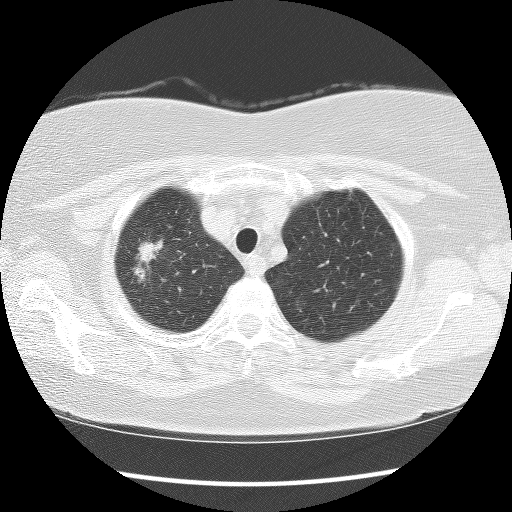
Axial slice from a low-dose chest CT screening exam; second screening round (one year after baseline); lung window (W 1500 / L -600 HU); 120 kVp; slice 5 of 79 in the series. Female participant, aged 67 years at enrolment.
- Expert reader's lesion annotation, bounding box <114,231,173,293> (left, top, right, bottom; pixels).
- The screening reader recorded 3 non-calcified nodules or masses ≥4 mm on this exam; which of them this box marks is not recorded.
- Later outcome: lung cancer diagnosed 56 days after this screen — adenocarcinoma with mixed subtypes, right upper lobe, poorly differentiated (G3), stage IA (AJCC 6th edition), 30 mm at pathology.